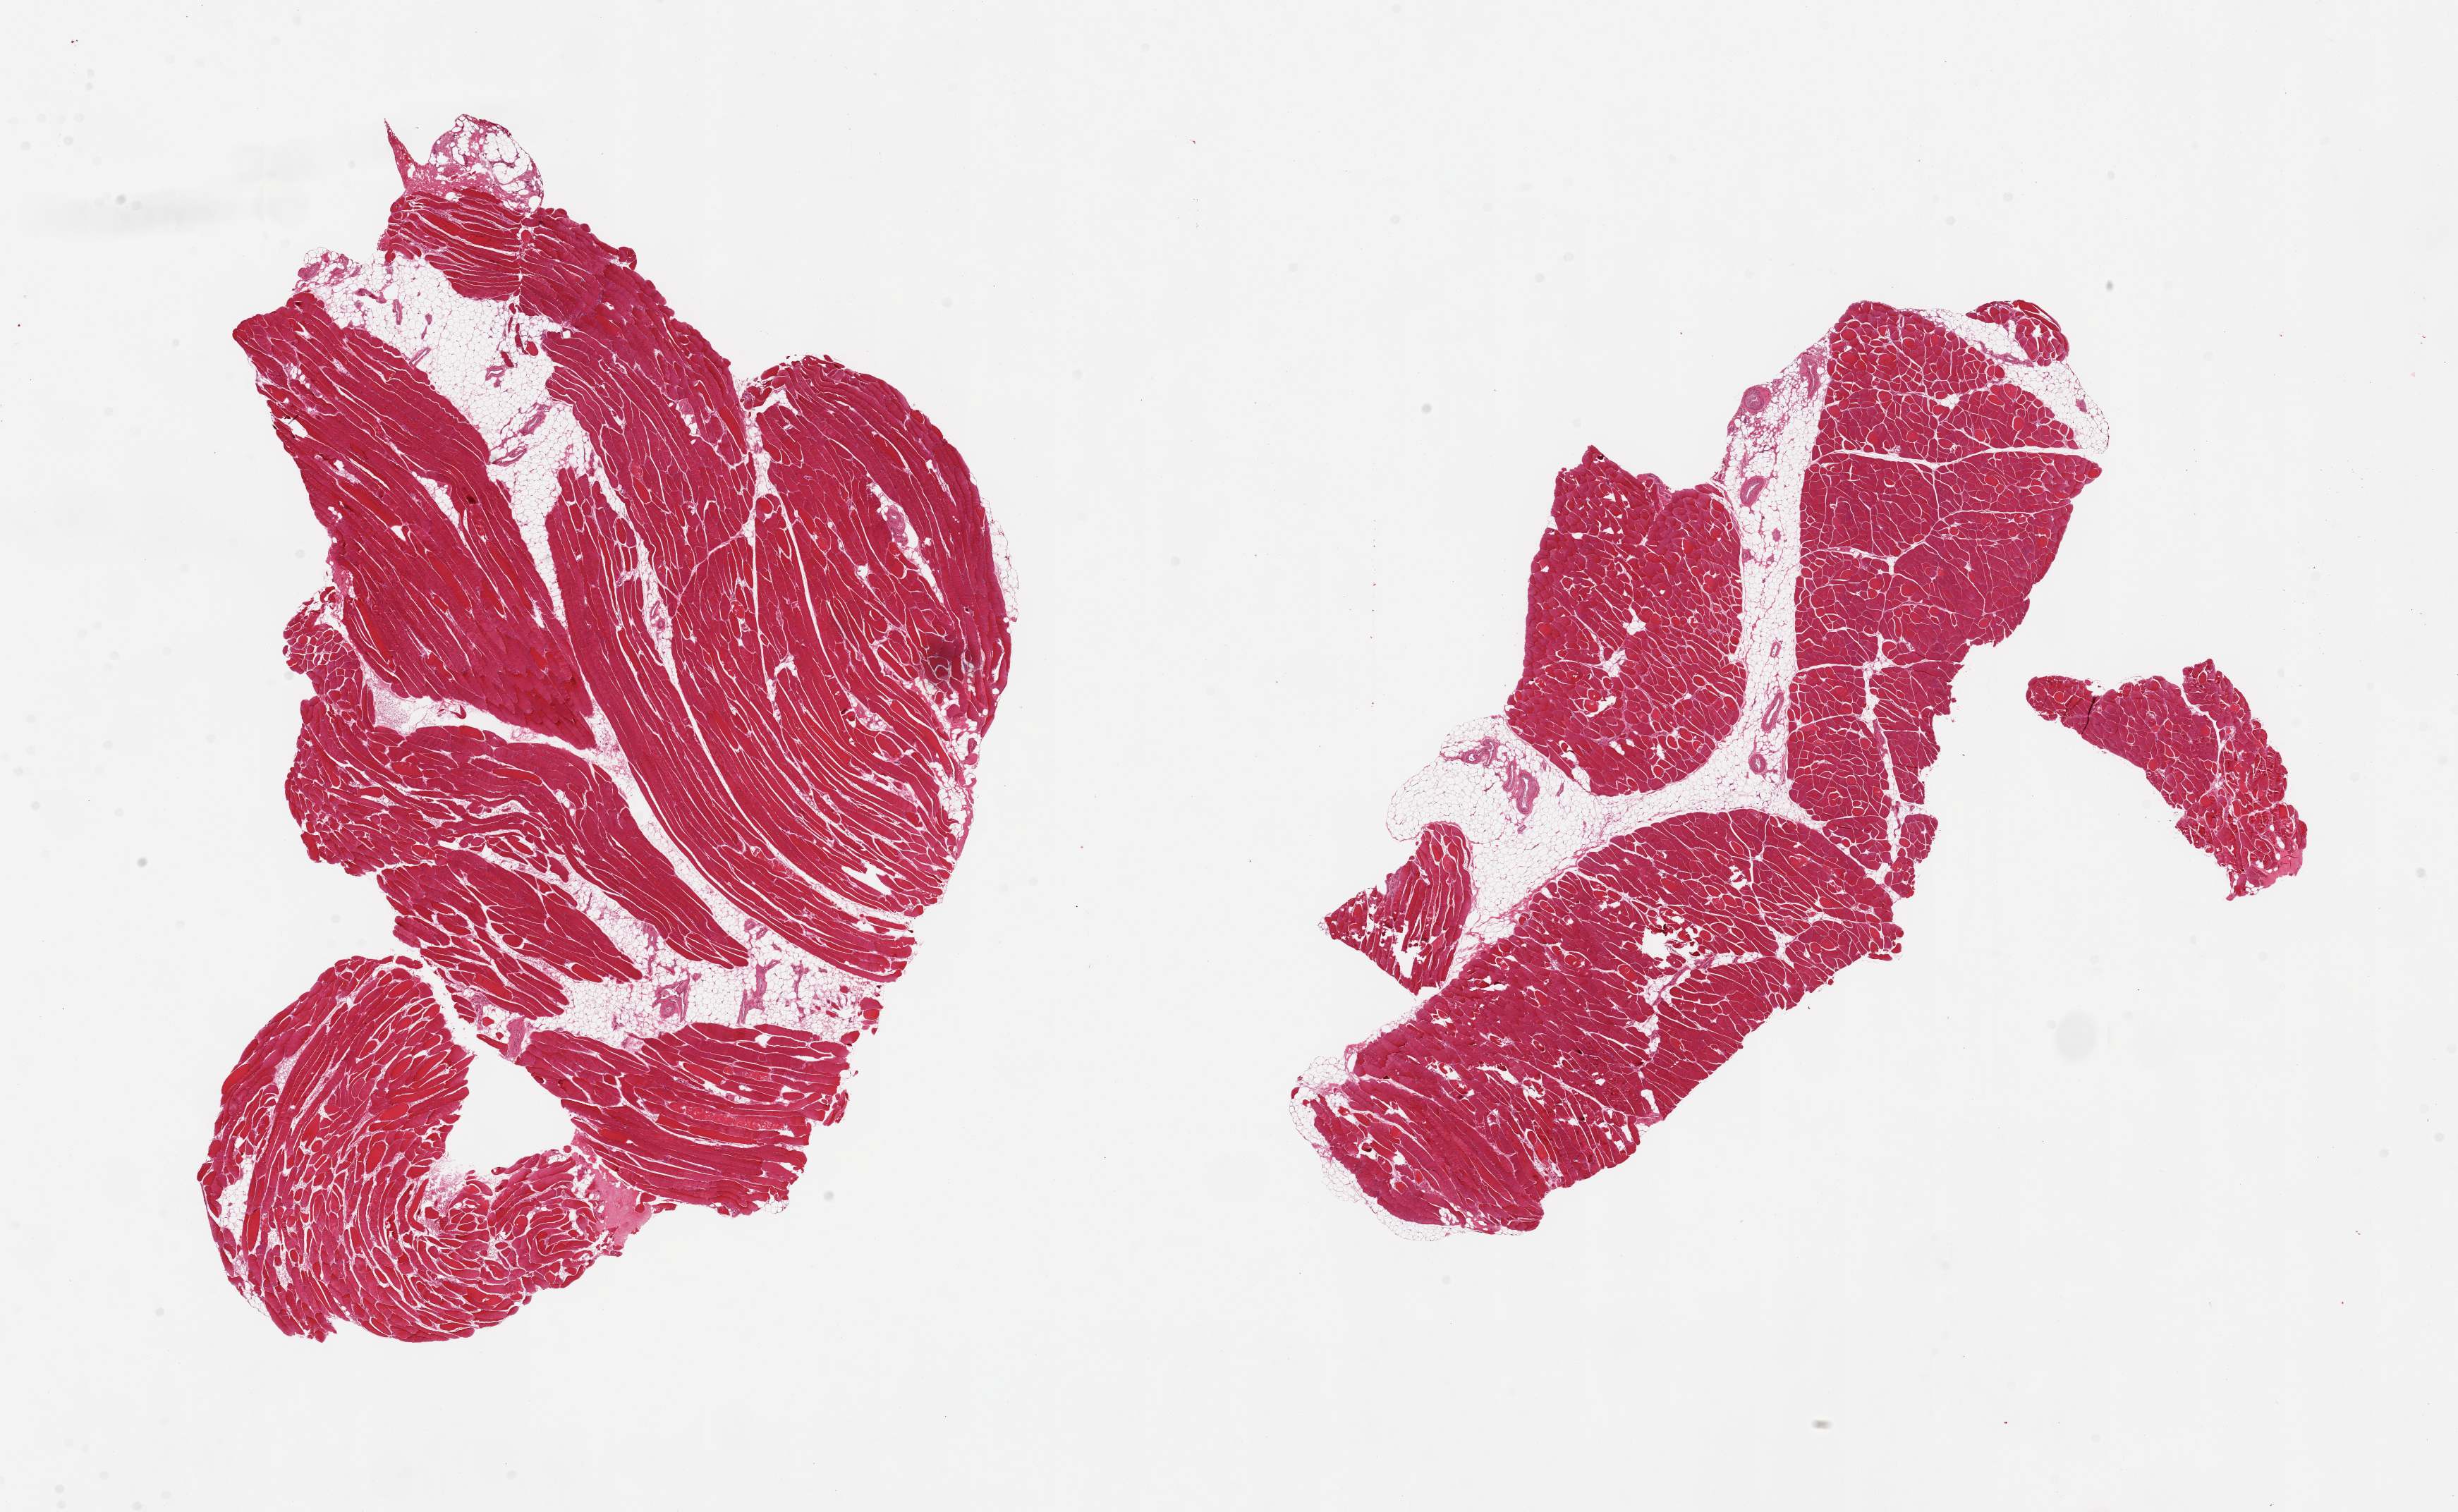
Whole-slide image, hematoxylin and eosin (H&E) stain, whole scanned area (about 27.6 x 17.0 mm) shown as a low-resolution overview, PAXgene-fixed, paraffin-embedded tissue, sampled site (target tissue): skeletal muscle, tissue donor sample. Male donor.
Pathologist's review note for this sample: 2 pieces, ~15-20% interstitial fat.